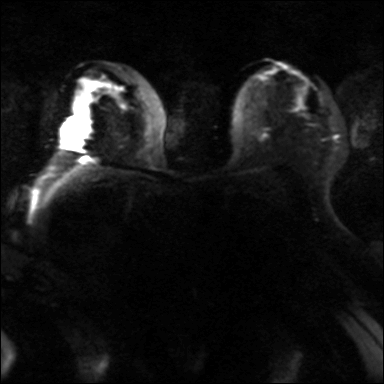
Breast MRI, one axial slice; slice 22 of 42 in the series (ordered by position); diffusion-weighted series; image 2 of 4 stored at this slice position (different b-values; order by instance number); 3 T; 384 × 384 image matrix, field of view 320 × 320 mm. Female patient.
Outlined on this slice (expert manual segmentation):
- tumour on diffusion-weighted imaging: box from (x=64, y=118) to (x=89, y=148) px